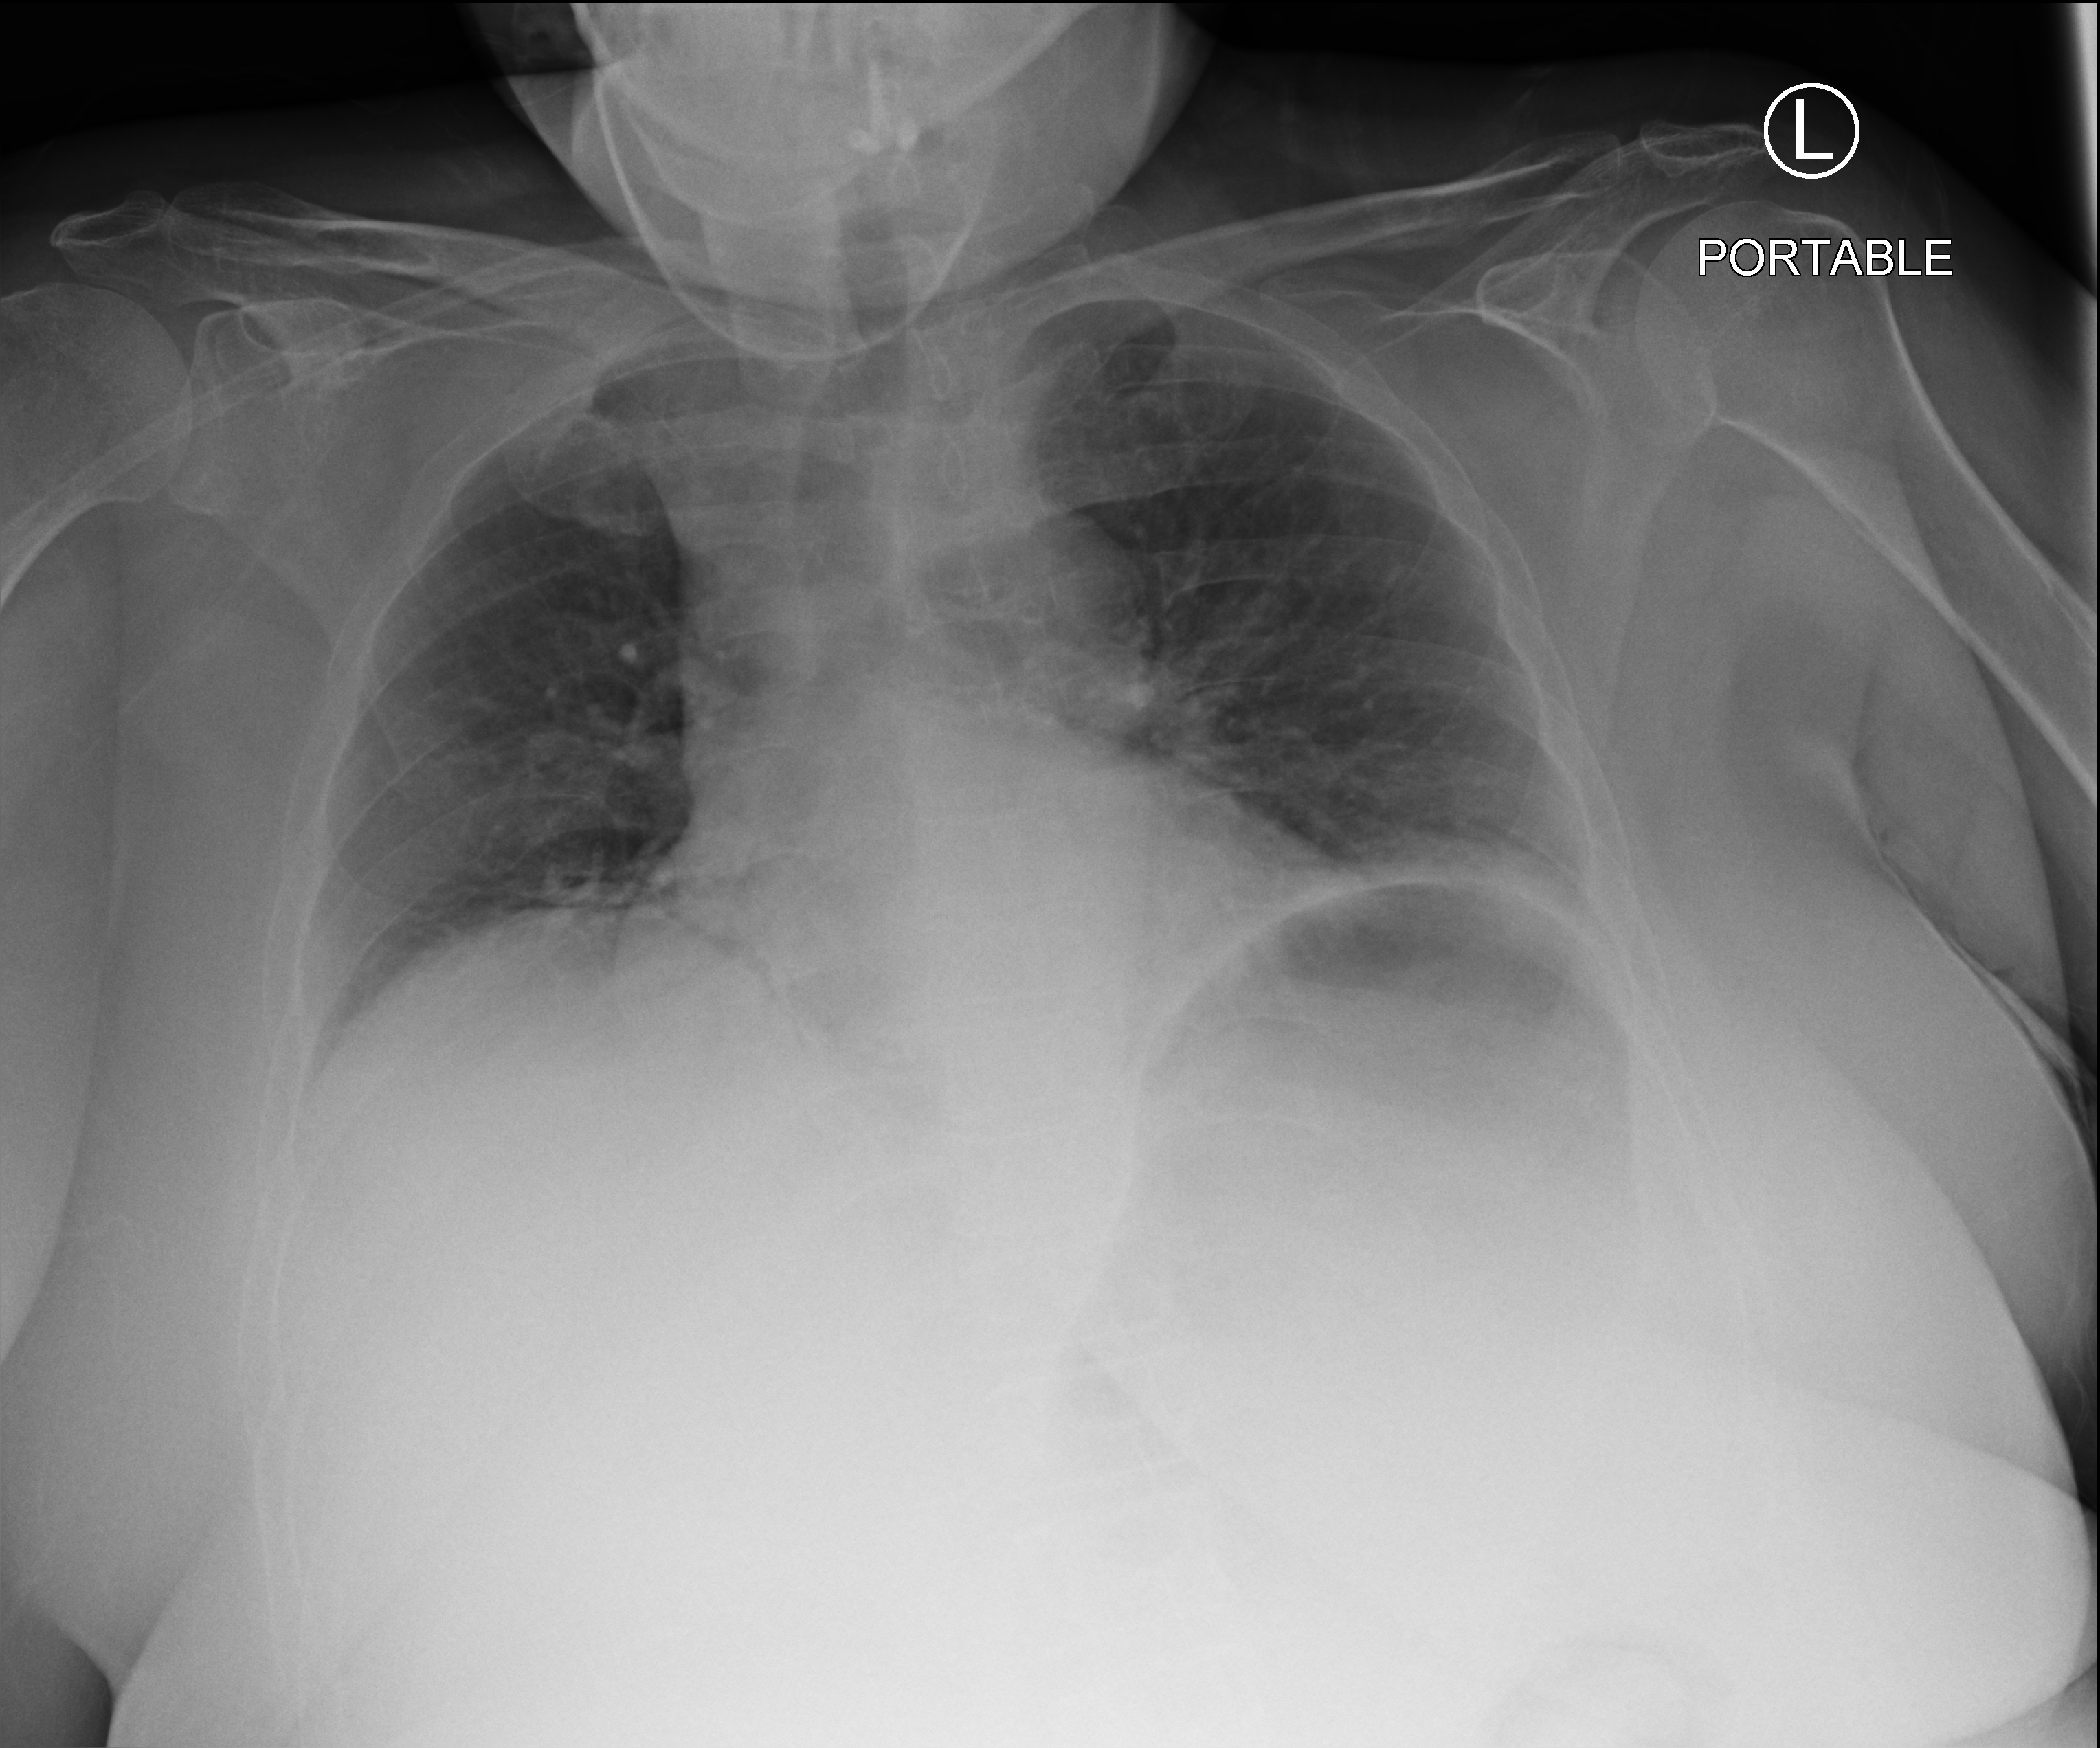
Chest X-ray (portable), anteroposterior (AP) projection. Patient hospitalised with COVID-19; female, aged 18–59 years.
Admission-level facts for this patient (not findings on this image; timing relative to this image not recorded):
- admitted to intensive care during this hospital stay: yes